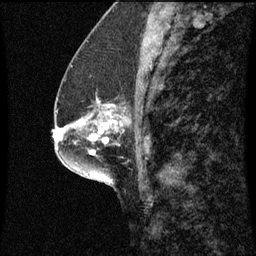
Breast MRI (dynamic contrast-enhanced), one sagittal slice. Slice 25 of 60 in the series (ordered by position). Dynamic contrast-enhanced series, image 2 of 3 at this slice position (ordered by acquisition). 1.5 T. TE 4.2 ms, TR 8.9 ms. 2 mm slice thickness. 256 × 256 image matrix, field of view 200 × 200 mm. Patient: female, 57 years. Case-level facts recorded for this patient, not image findings: setting: breast cancer imaged before/during neoadjuvant chemotherapy; receptor status: HR-positive, HER2-negative.
Structures marked on this image (semi-automatic segmentation, software-assisted and operator-edited):
- analysis volume of interest (the breast-tissue region the enhancement analysis was run in; not a lesion): bounding box <82,96,124,125> (left, top, right, bottom; pixels)
- tumour enhancement mask (voxels above the 70 % enhancement threshold inside the analysis volume of interest): <110,120,118,123>